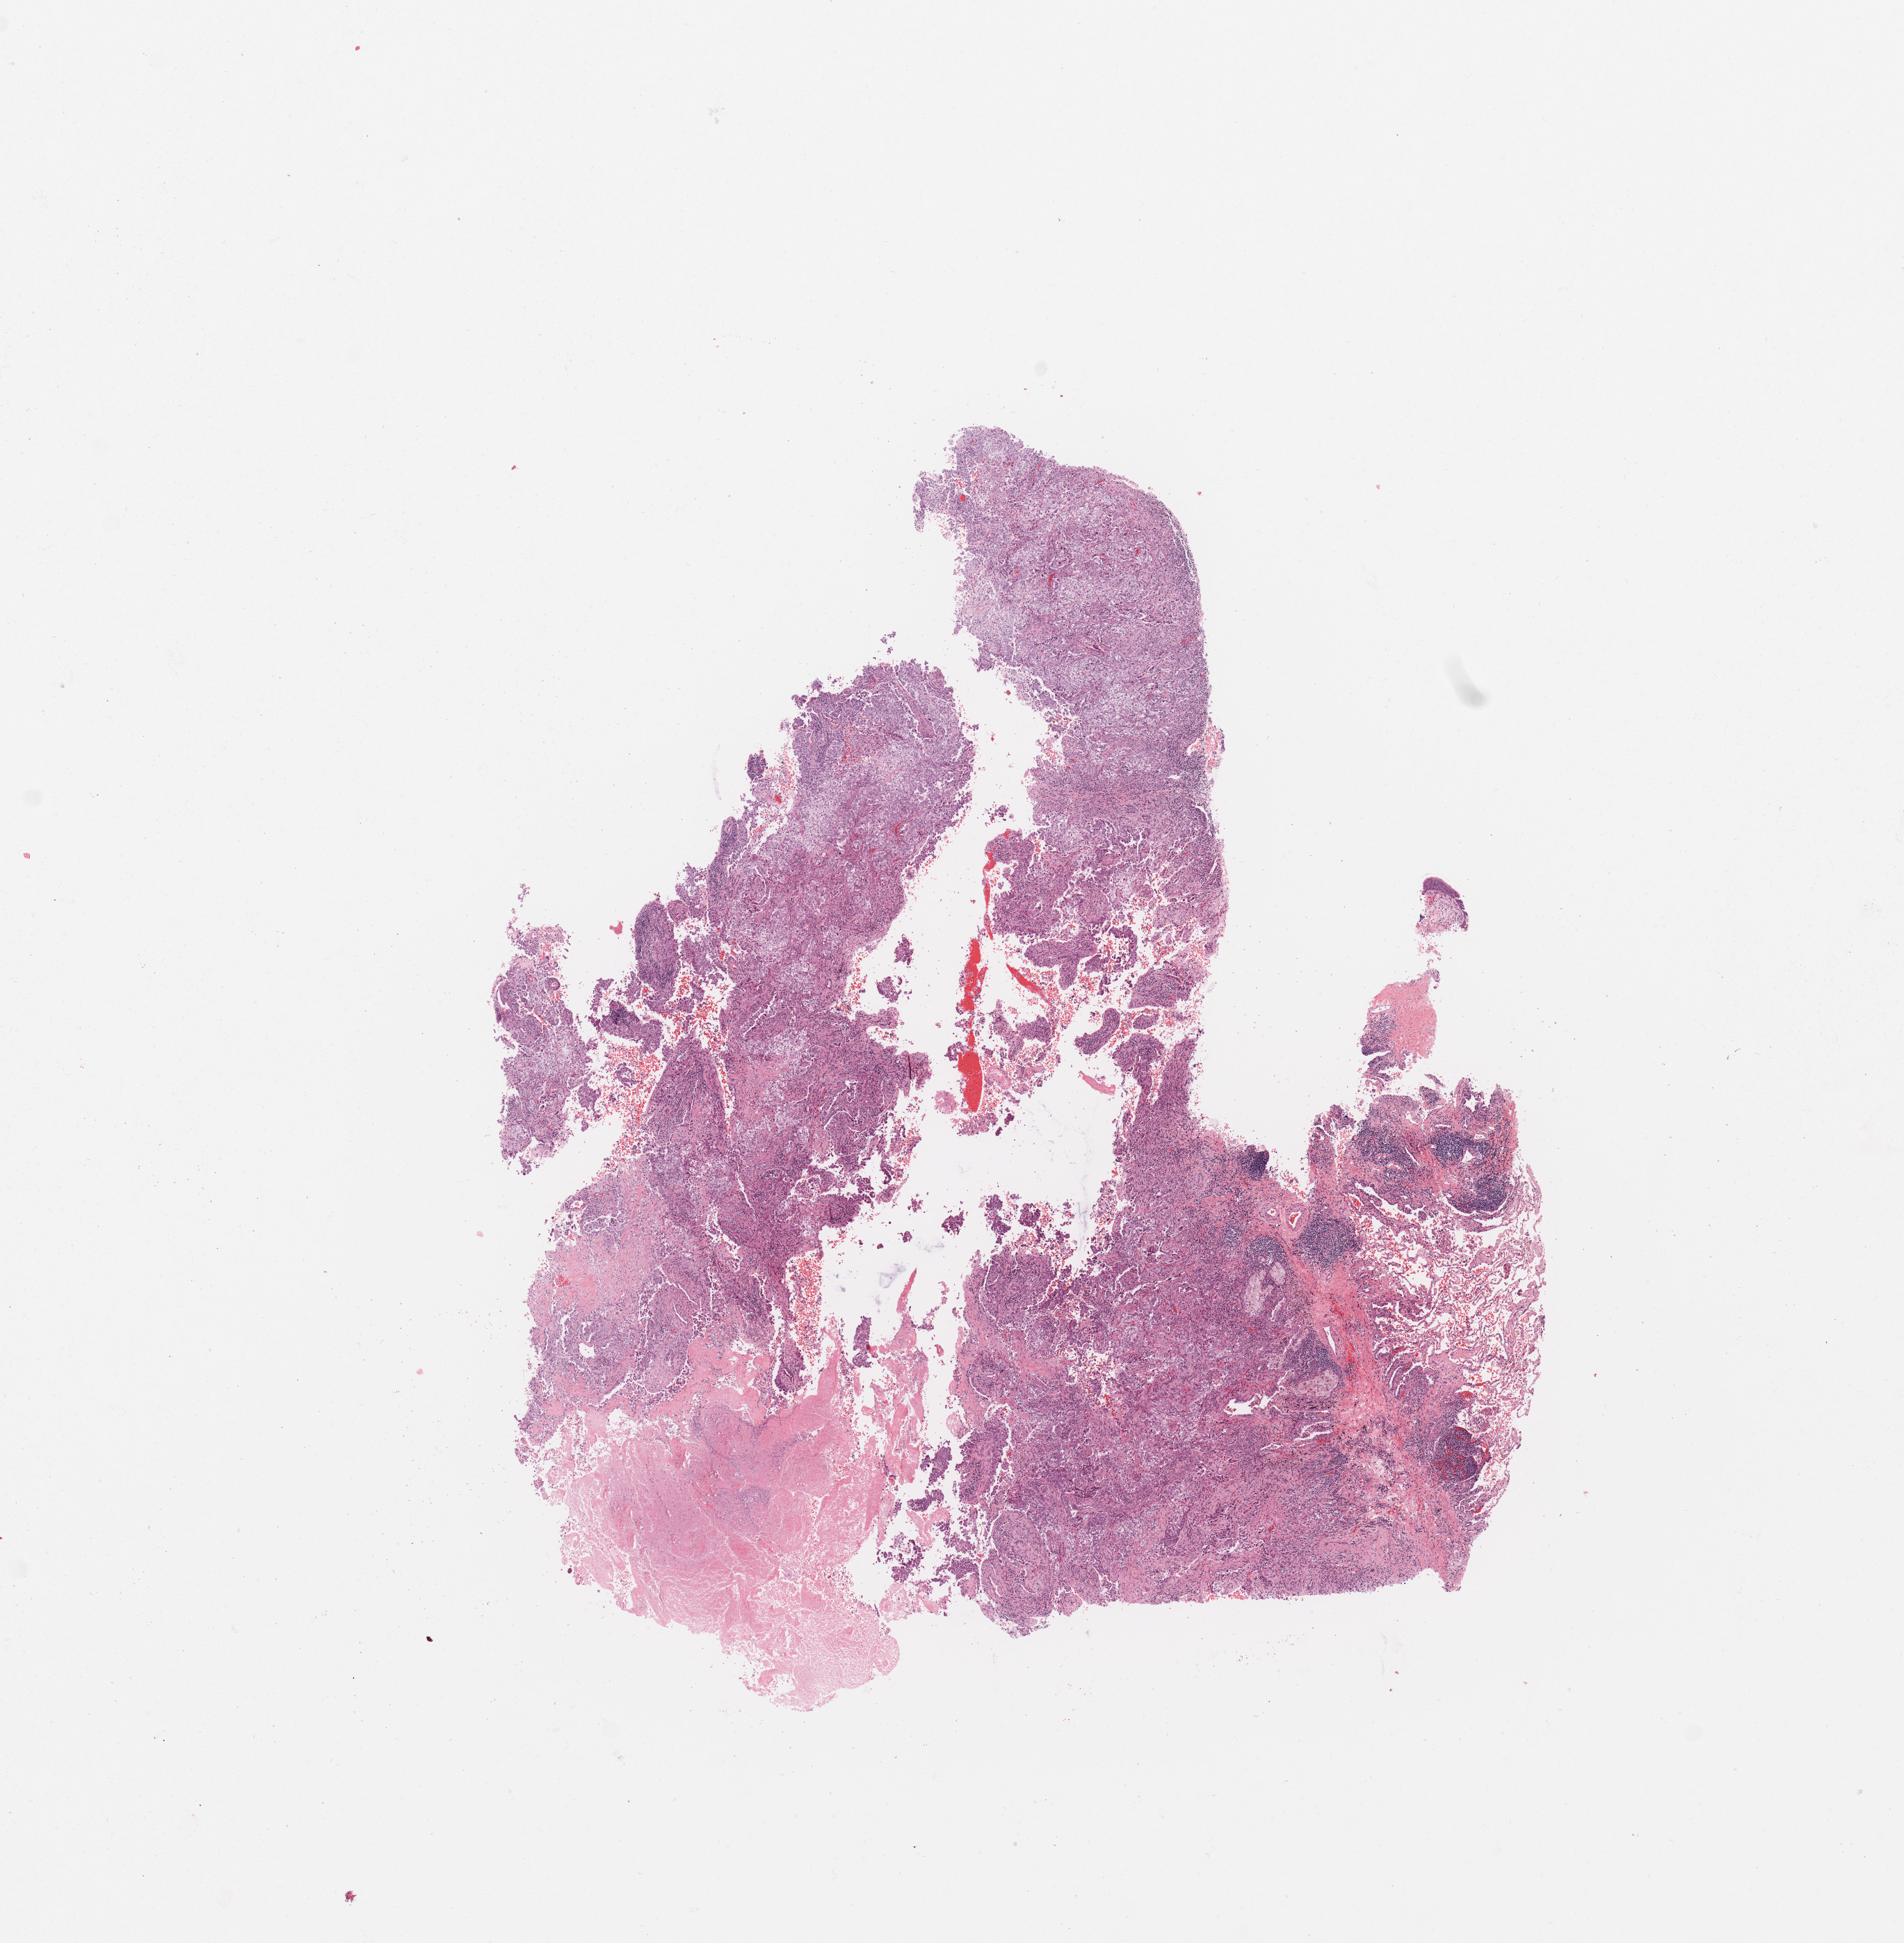
Digitized Hematoxylin and eosin (H&E) stained tissue section (whole slide) — low-resolution overview of the scanned area, about 10.8 x 11.0 mm, tumour tissue sample, sampled site: lung. Patient: male, age 70 years. Histologic grade: G3 (poorly differentiated). Slide review estimates, as recorded: tumour nuclei 65%, necrosis 7%.
Diagnosis: Adenocarcinoma, NOS. AJCC pathologic stage: IA. Primary tumour site (as recorded): left upper lobe.